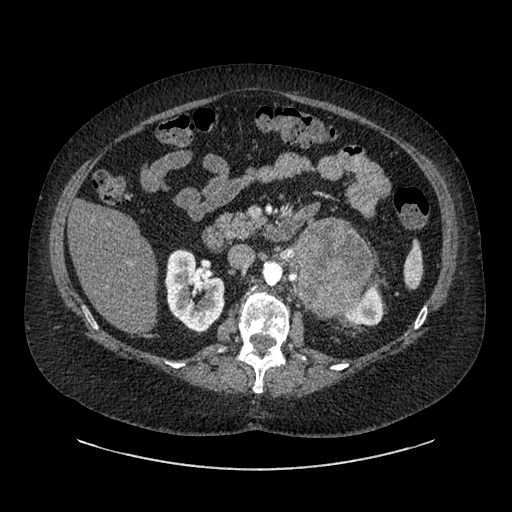
Contrast-enhanced abdominal CT, one axial slice. Position 525 of 769 along the scan axis. 120 kVp. Intravenous contrast given. Soft-tissue window (W 400 / L 40 HU). 0.62 mm slice thickness. 512 × 512 image matrix, field of view 460 × 460 mm. Patient: female, 61 years. Case-level facts recorded for this patient, not image findings: diagnosis: adrenocortical carcinoma; tumour side: left adrenal; tumour size at pathology: 13 cm; Ki-67 index: 79 %; stage (as recorded): 2.
Structures marked on this image (semi-automatically segmented with operator editing):
- mass: bounding box (x1, y1, x2, y2) in pixels: (296, 221, 380, 311)